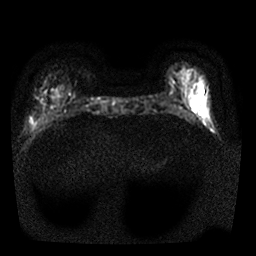
Breast MRI, one axial slice. Diffusion-weighted series; image 2 of 4 stored at this slice position (different b-values; order by instance number). 1.5 T. 4 mm slice thickness. 256 × 256 image matrix, field of view 310 × 310 mm. Female patient.
Annotated regions visible in this slice (outlined manually by an expert reader):
- tumour on diffusion-weighted imaging: bounding box <34,95,40,100> (left, top, right, bottom; pixels)